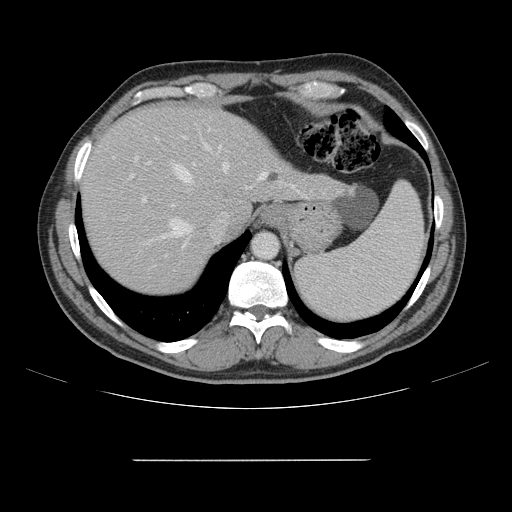
Contrast-enhanced abdominal CT, one axial slice. Soft-tissue window (W 400 / L 40 HU). 512 × 512 image matrix. Male patient, age 54 years. From the clinical record (not read from this slice): diagnosis: colorectal cancer liver metastases, imaged before liver resection; multiple liver metastases: yes; largest metastasis: 1 cm; disease in both lobes: no.
Annotated regions visible in this slice (manually delineated by an expert):
- hepatic veins: bounding box [x1, y1, x2, y2] px = [151, 144, 308, 241]
- liver: [83, 106, 340, 293]
- planned liver remnant (the part of the liver to remain after resection): [82, 106, 255, 292]
- portal vein (with intrahepatic branches): [113, 136, 221, 272]
- liver metastasis: [268, 173, 280, 183]